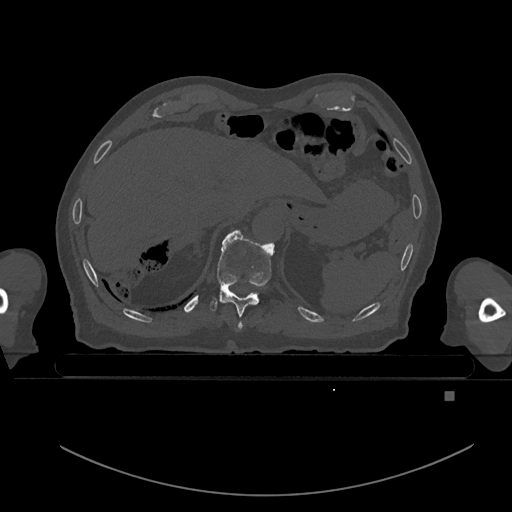
CT including the spine, one axial slice. Bone window (W 1800 / L 400 HU). 0.5 mm slice thickness. 512 × 512 image matrix, field of view 456 × 456 mm. Male patient, age 82 years. Case-level facts recorded for this patient, not image findings: primary cancer: prostate; vertebrae with lytic lesions (as recorded): T11, T9, T8, T2.
Structures marked on this image (semi-automatically segmented with operator editing):
- T10 vertebra: bounding box (x1, y1, x2, y2) in pixels: (209, 231, 274, 327)